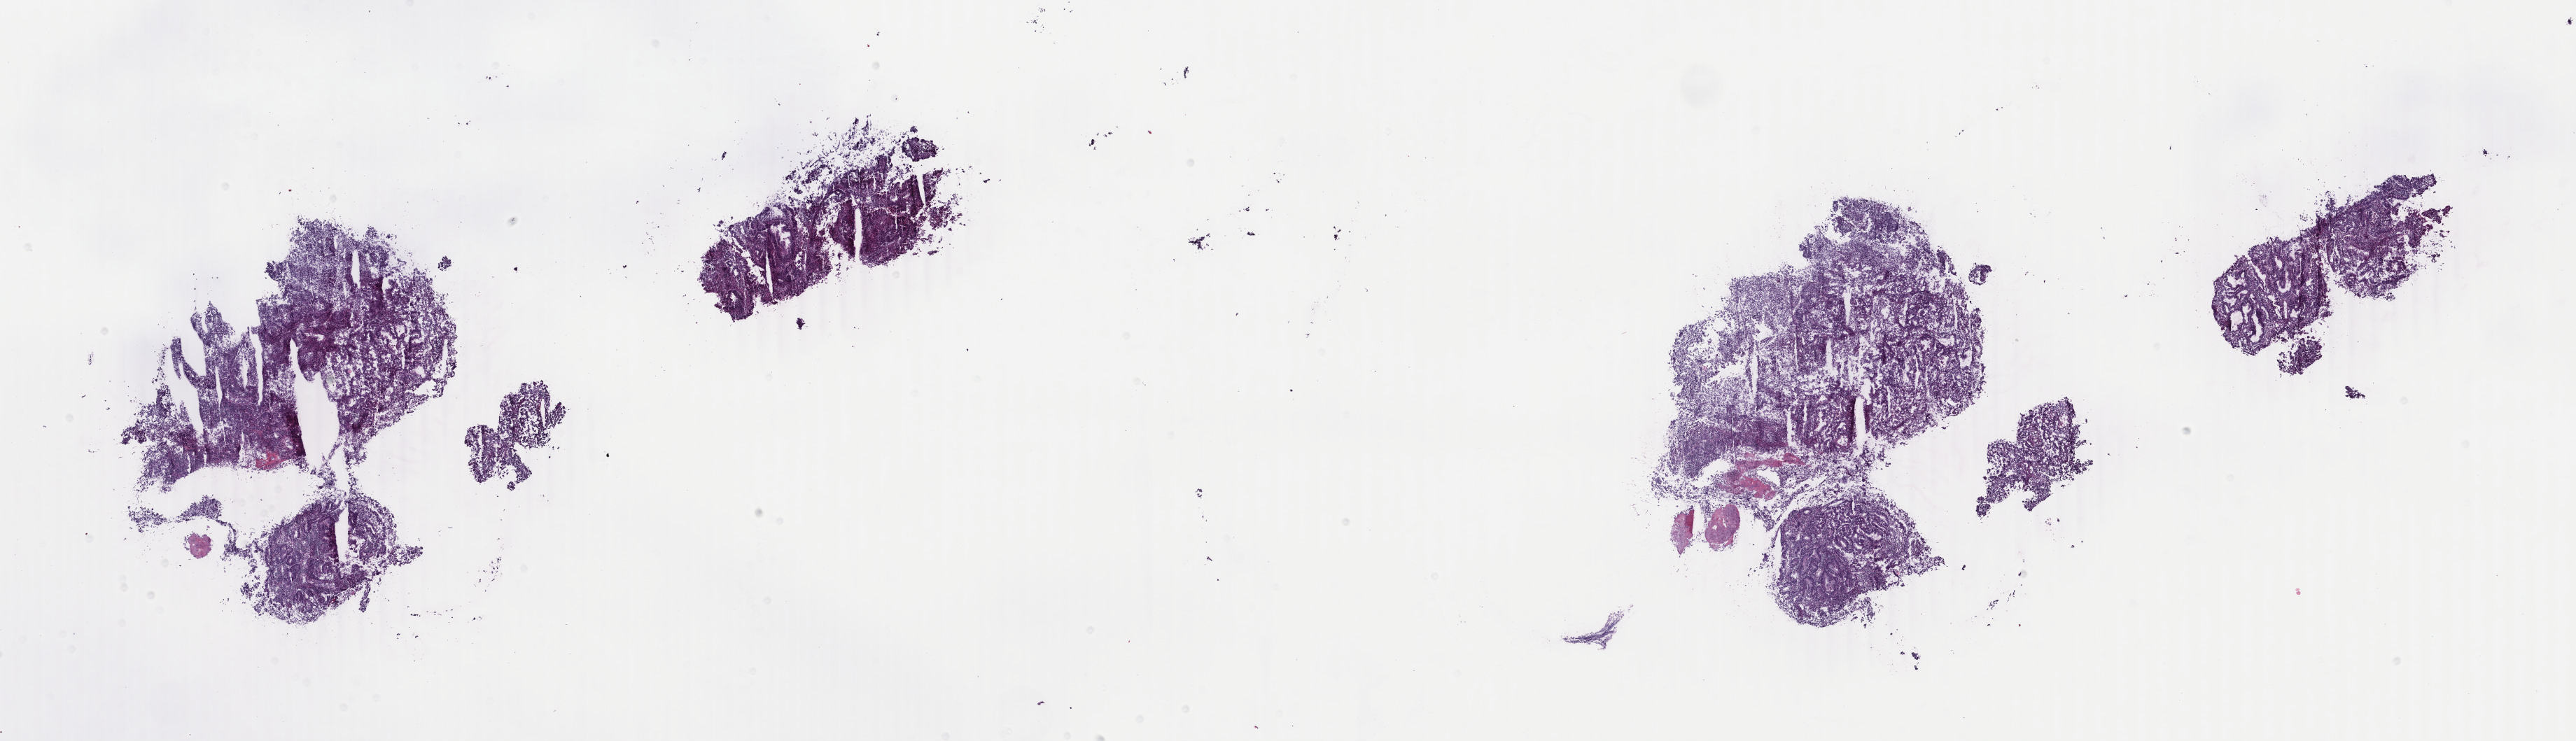
Whole-slide histology image, H&E-stained — whole scanned area (about 29.3 x 8.4 mm, from a 40x scan) shown as a low-resolution overview. Frozen section. Uterus, primary tumour sample. Female, age 54 years at initial diagnosis. Histologic grade: G1 (well differentiated). Slide review estimates, as recorded: tumour cells 100%, tumour nuclei 80%, normal cells 0%, stromal cells 0%, necrosis 0%. Inflammatory infiltration, as recorded: lymphocyte infiltration 0%, monocyte infiltration 0%, neutrophil infiltration 0%.
Pathologic diagnosis: Endometrioid adenocarcinoma, NOS (endometrium). FIGO stage: IA.